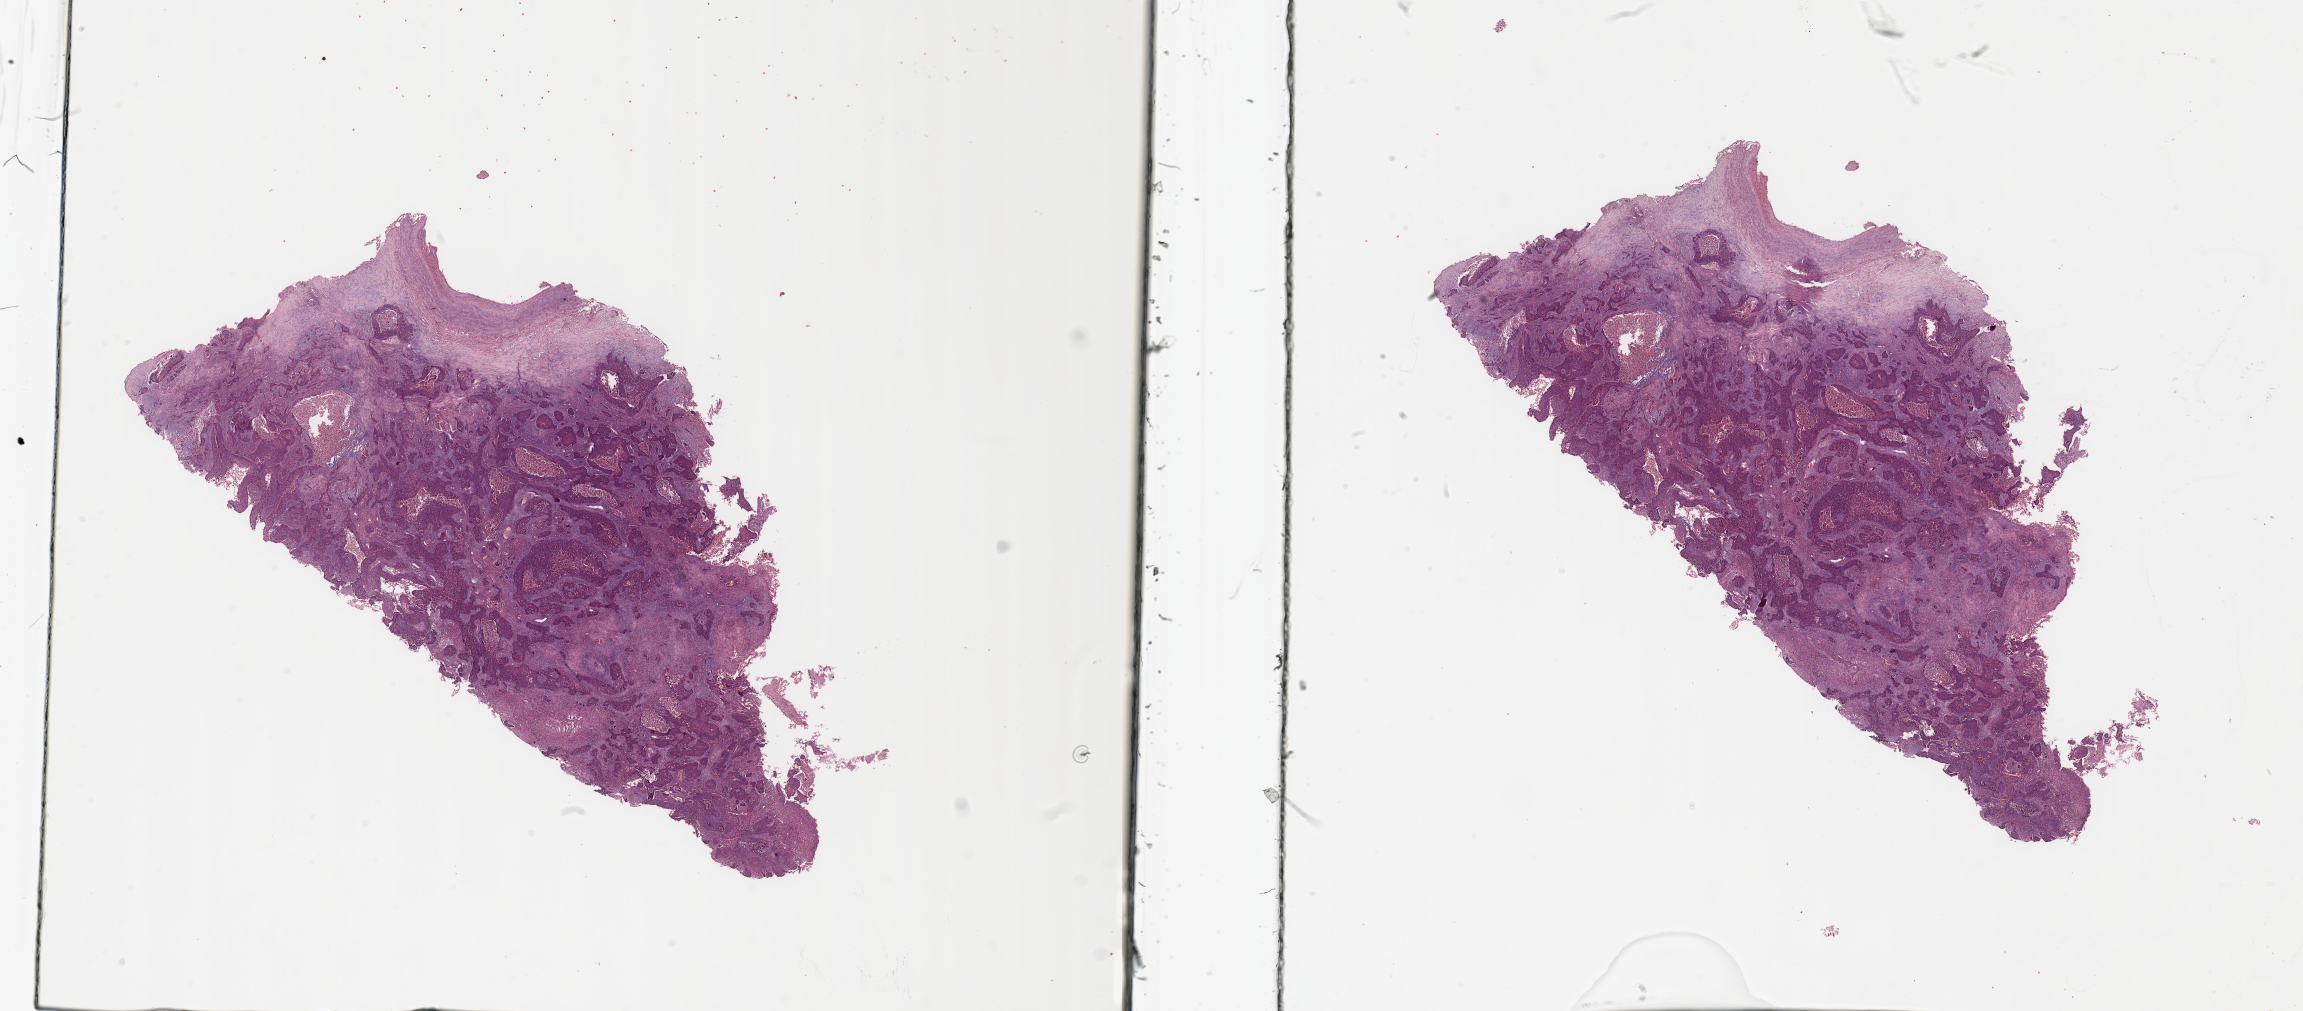
Digitized H&E-stained tissue section (whole slide) — whole scanned area (about 36.4 x 16.0 mm) shown as a low-resolution overview. Lung, tumour tissue. Male, 64 y/o. Histologic grade: G2 (moderately differentiated).
Histologic diagnosis: Squamous cell carcinoma, NOS. AJCC pathologic stage: IIA.